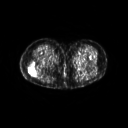
FDG PET of an extremity soft-tissue mass (from a PET/CT study), one axial slice; position 24 of 267 along the scan axis; 3.27 mm slice thickness; 128 × 128 image matrix. Female patient, age 57 years. From the clinical record (not read from this slice): histological type: epithelioid sarcoma with vascular differentiation; site of the primary tumour: right buttock.
Structures marked on this image (expert contour drawn on MRI and transferred to this co-registered scan by the dataset authors):
- gross tumour volume (mass): bounding box <32,64,34,65> (left, top, right, bottom; pixels)